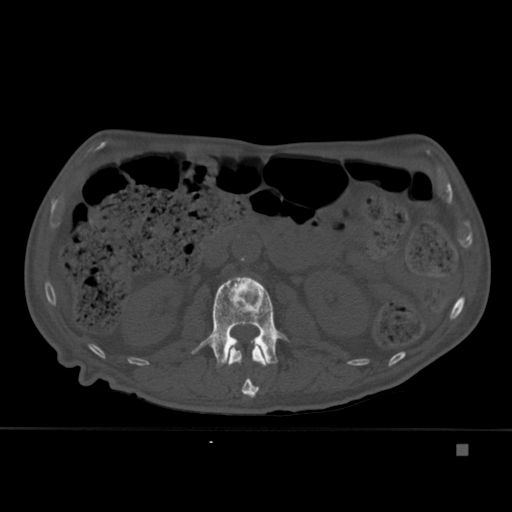
CT including the spine, one axial slice; position 167 of 451 along the scan axis; bone window (W 1800 / L 400 HU); 1.5 mm slice thickness; 512 × 512 image matrix. Male patient, age 75 years. Case-level facts recorded for this patient, not image findings: primary cancer: prostate.
Outlined on this slice (semi-automatically segmented with operator editing):
- L1 vertebra: bounding box (x1, y1, x2, y2) in pixels: (228, 345, 268, 398)
- L2 vertebra: (191, 277, 289, 368)